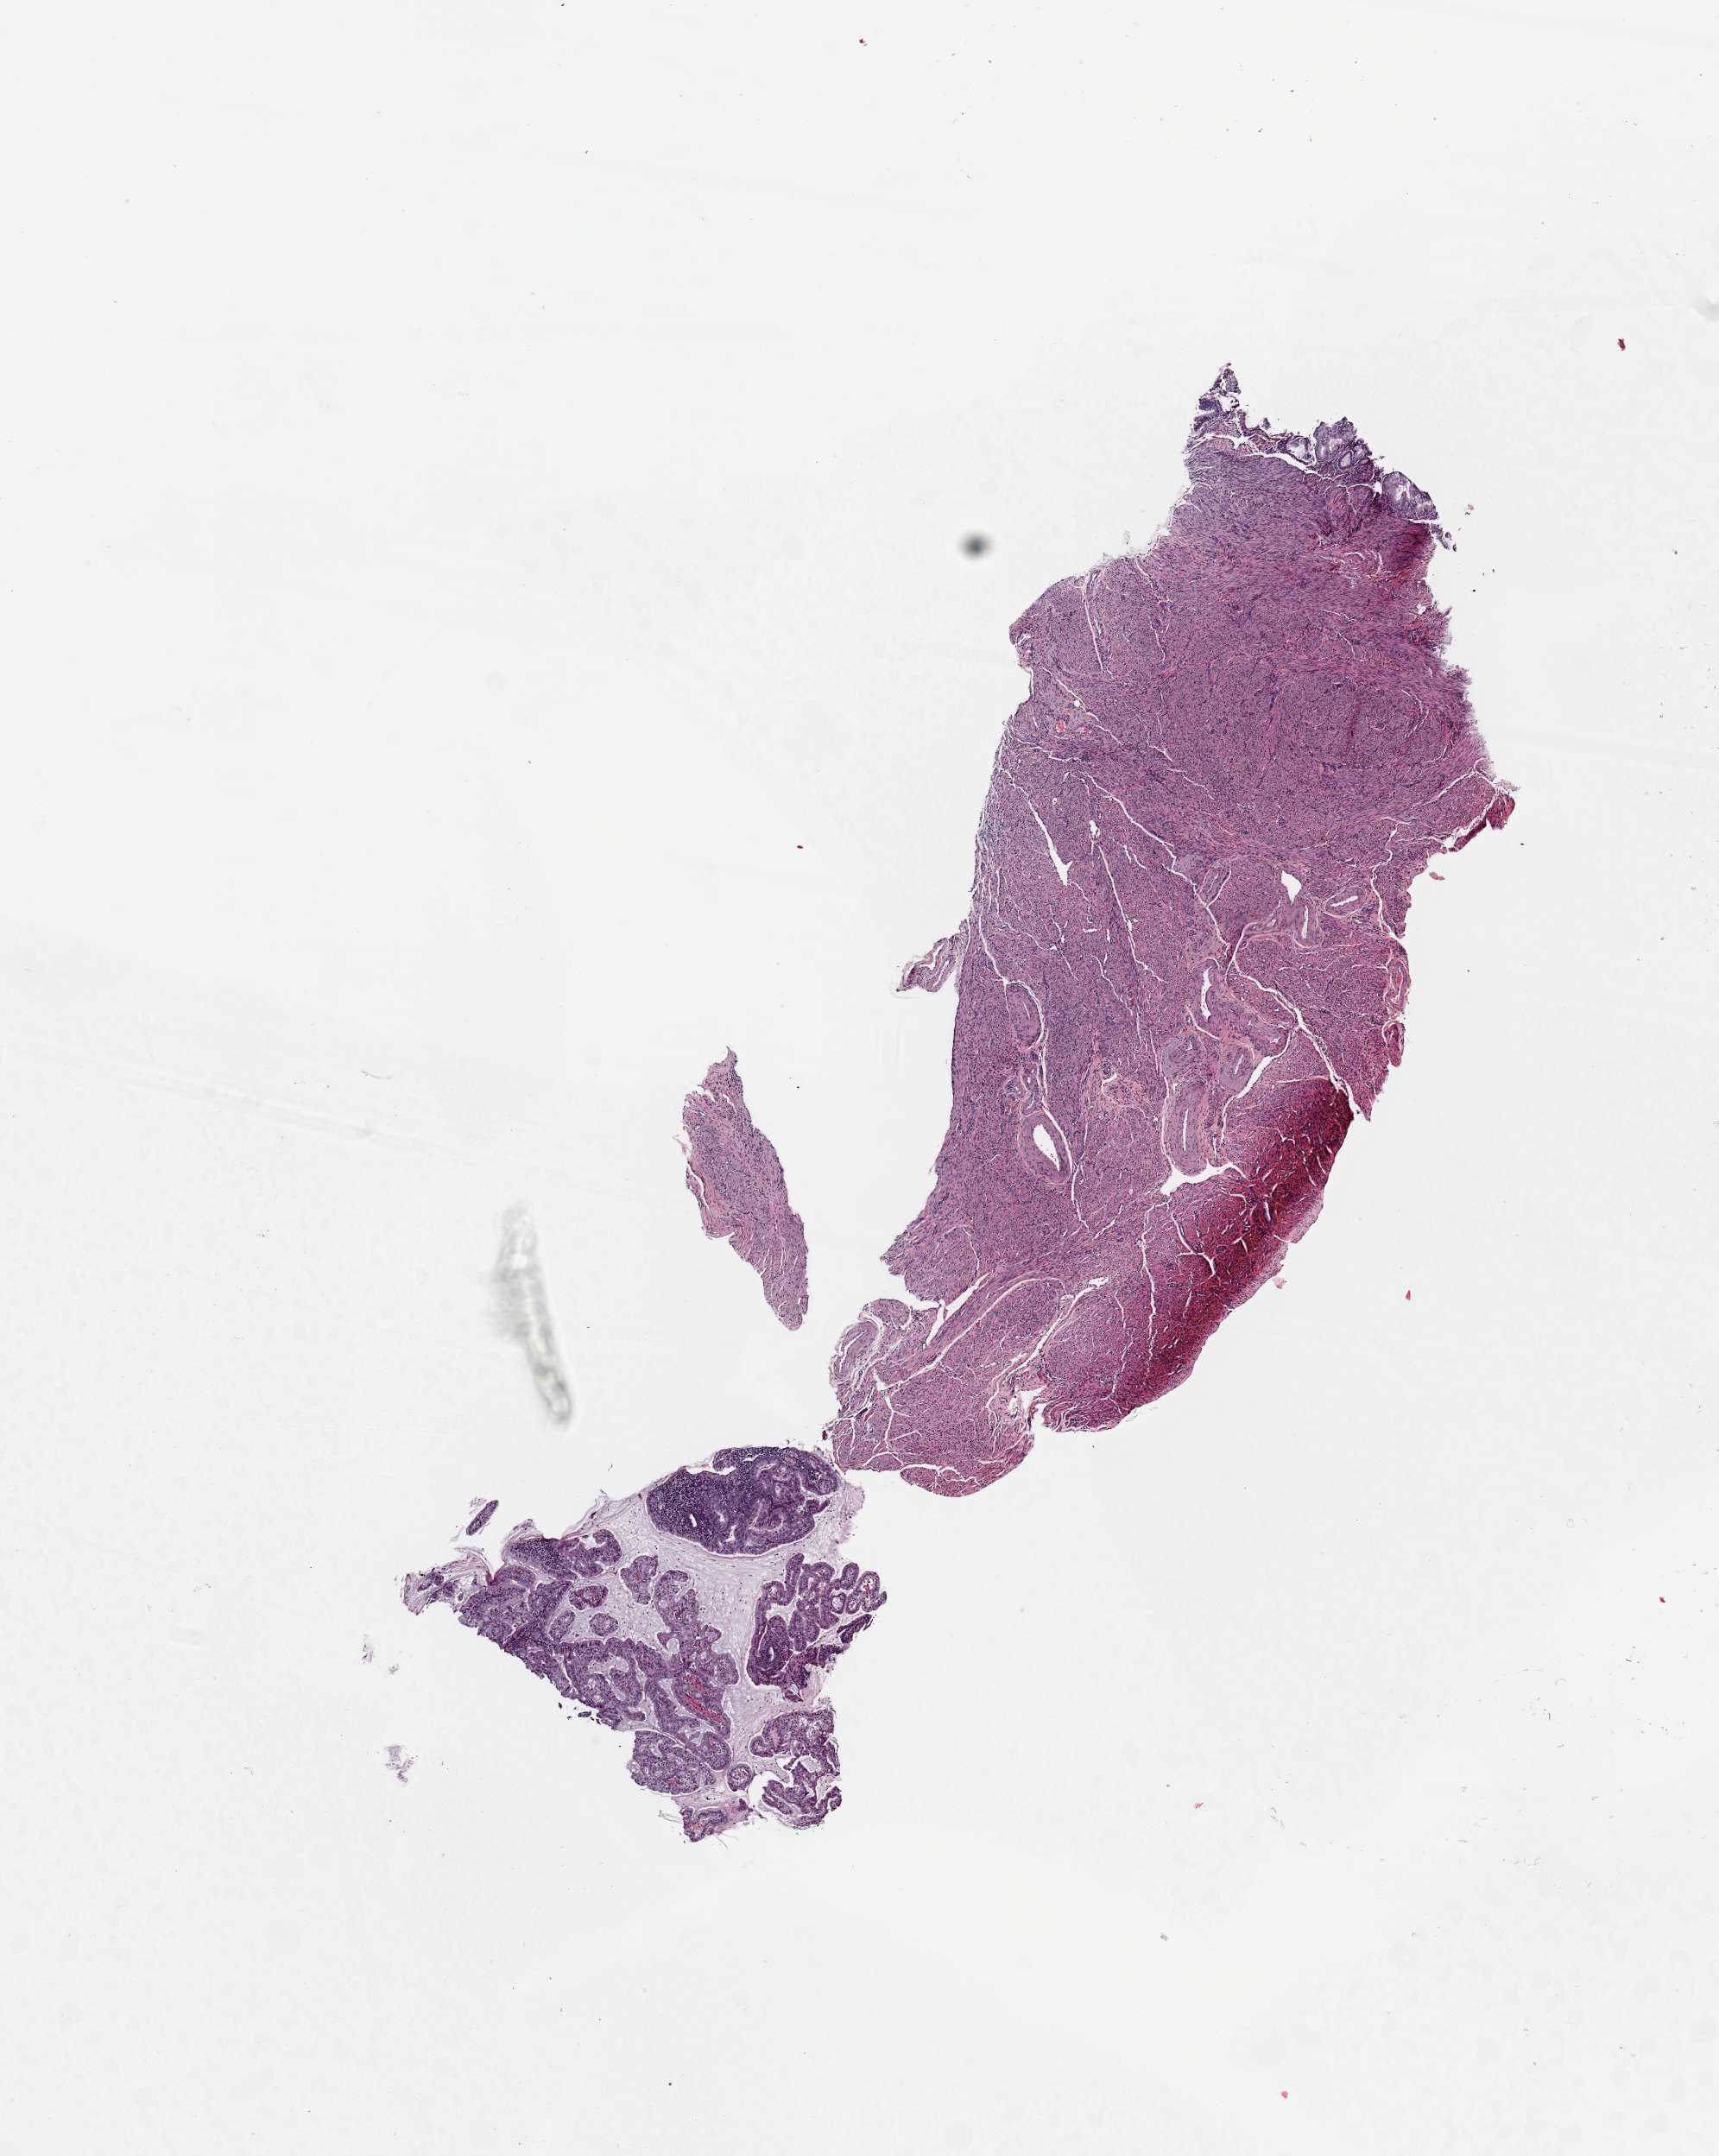
Whole-slide histology image, Hematoxylin and eosin (H&E) stained — a low-resolution overview of the entire scanned area, about 7.9 x 9.9 mm (slide scanned at 20x), tumour tissue sample, uterus. 69-year-old female patient. Histologic grade: G2 (moderately differentiated).
- AJCC pathologic stage: IA
- diagnosis: Endometrioid adenocarcinoma, NOS